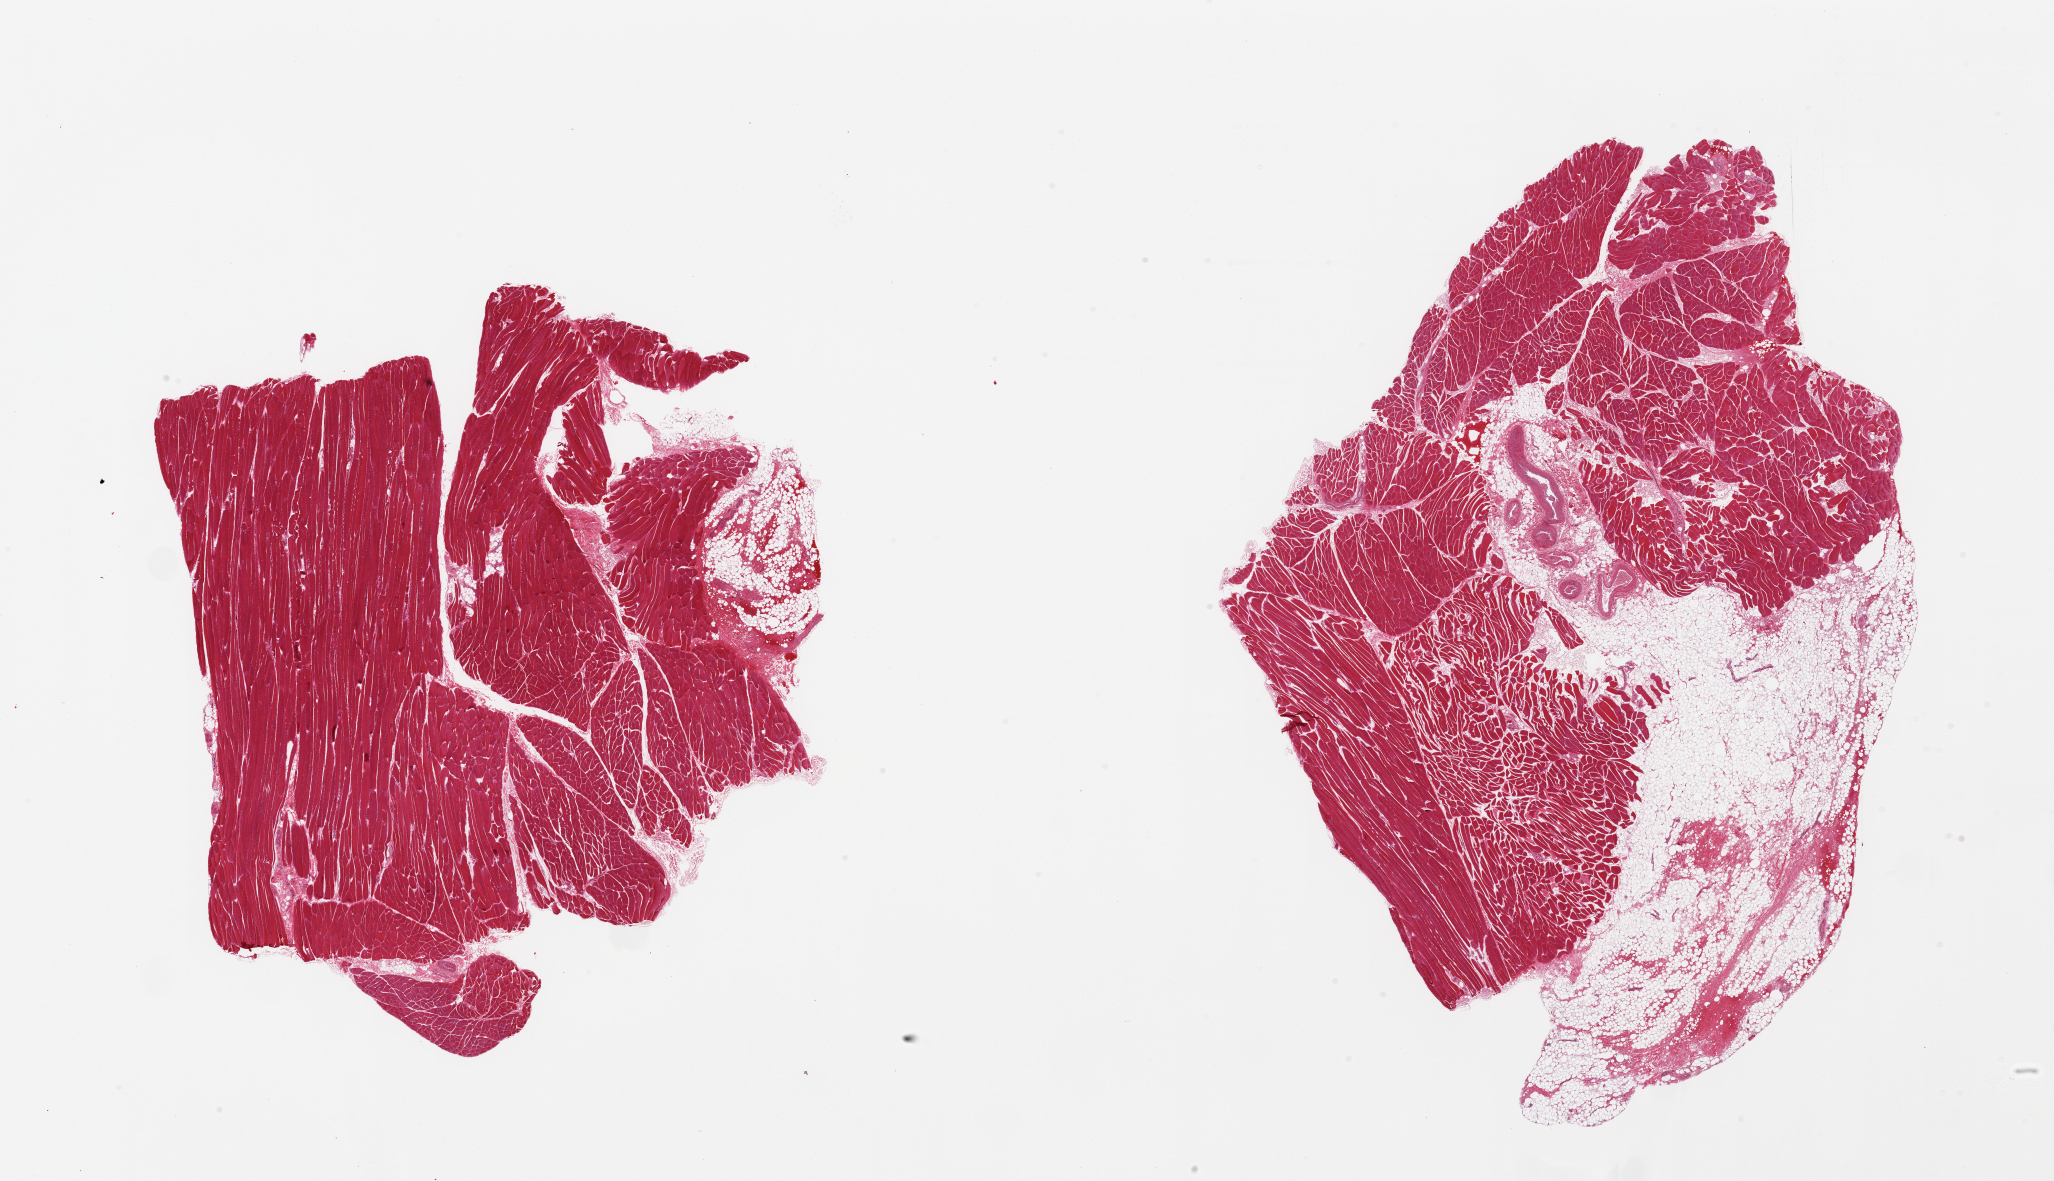
Whole-slide image, haematoxylin and eosin stain — shown as a low-resolution overview of the whole scanned area (about 32.5 x 18.7 mm, slide scanned at 20x), PAXgene-fixed paraffin-embedded (PFPE) section, sampled site (target tissue): skeletal muscle, tissue donor sample. Male donor.
Pathologist's review note for this sample: 2 pieces, ~20-25%% adherent or interstitlal fat/vascular elements.